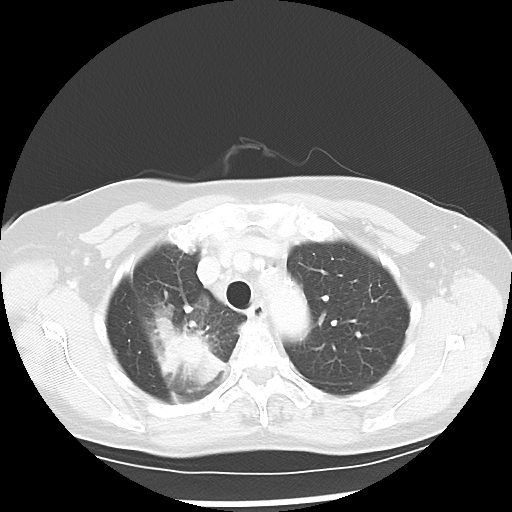
Chest CT, one axial slice; position 40 of 52 along the scan axis; reconstruction kernel LUNG; lung window (W 1500 / L -600 HU); 512 × 512 image matrix, field of view 328 × 328 mm. Patient: female, 60 years. Case-level facts recorded for this patient, not image findings: clinical TNM (as recorded): T2 N1 M1a.
Annotated regions visible in this slice (bounding box drawn by a radiologist):
- lung tumour (recorded histology: adenocarcinoma): bounding box <146,302,226,398> (left, top, right, bottom; pixels)